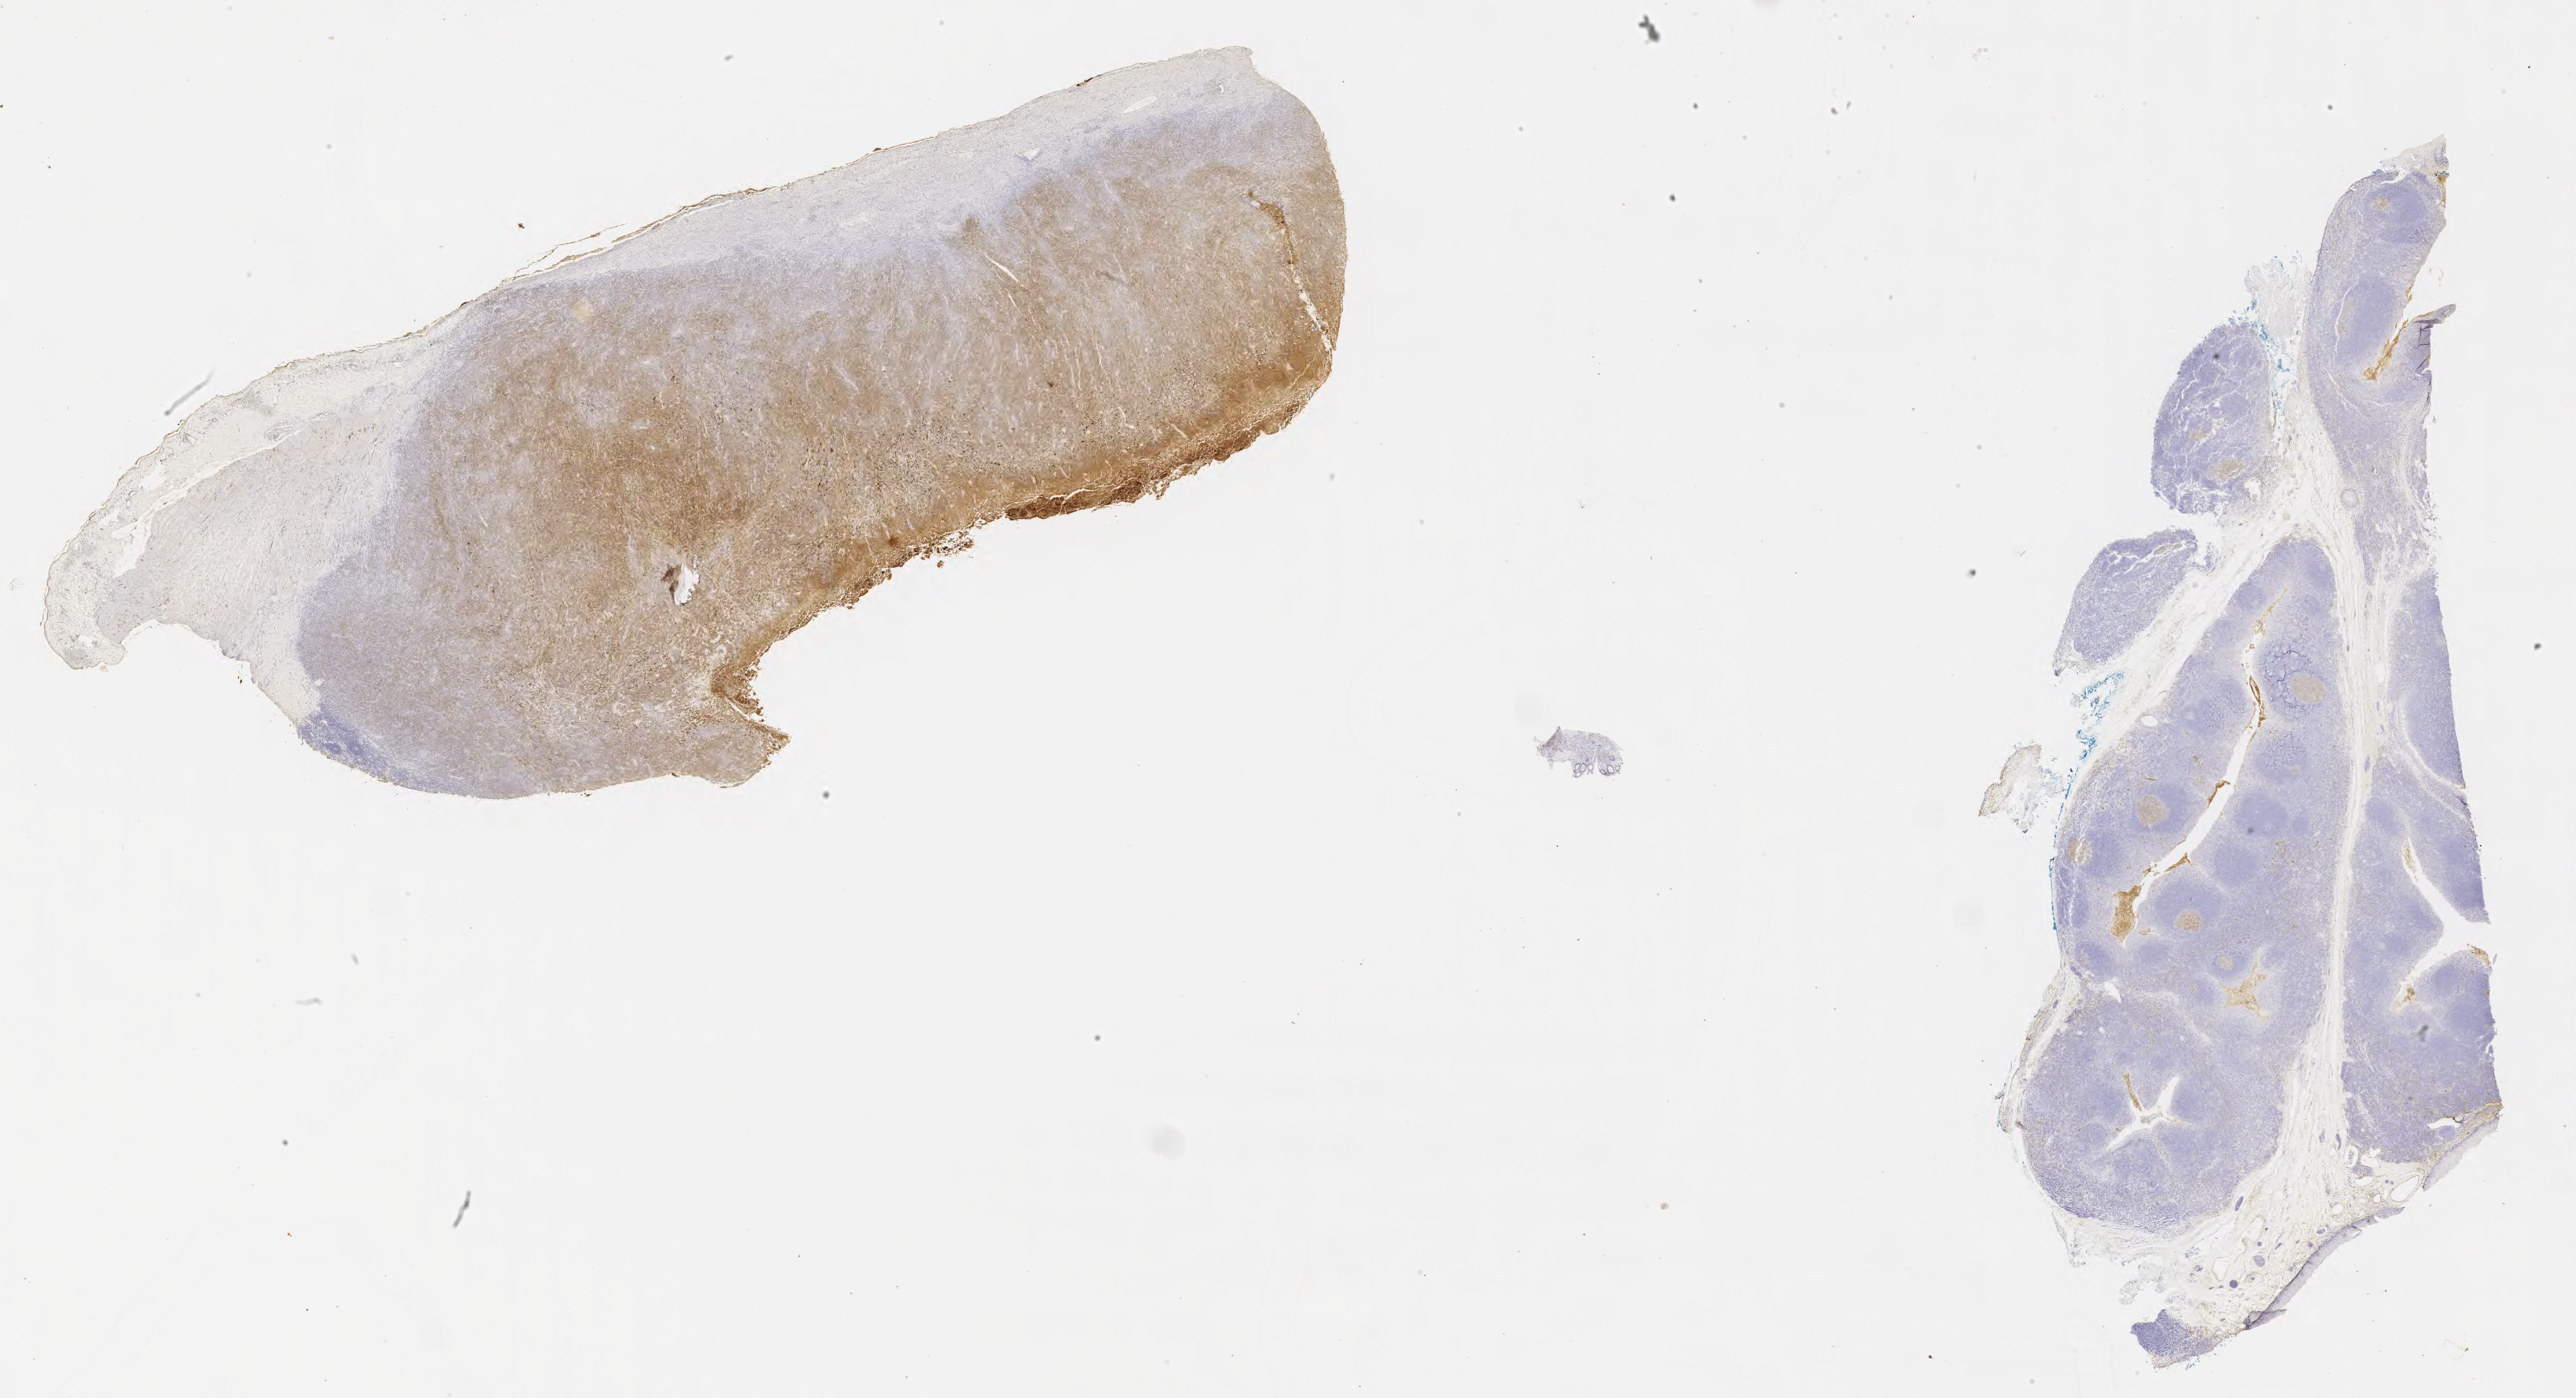
Whole-slide image, immunohistochemical stain for CD10 — low-resolution overview of the scanned area, about 30.2 x 16.4 mm. Specimen: tumor tissue. Anatomic site: small intestine. Male patient; age at initial diagnosis 3 years.
- diagnosis: Burkitt lymphoma, NOS